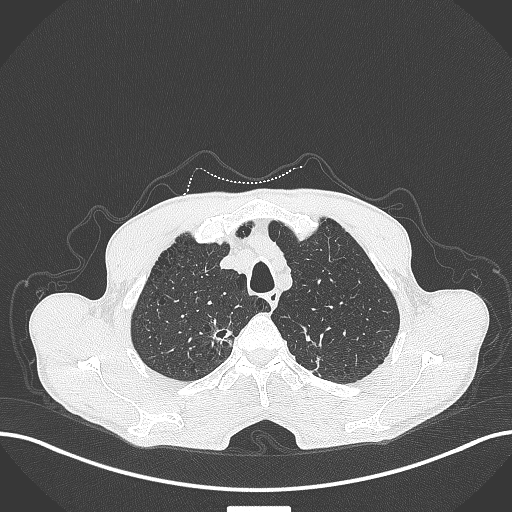
Chest CT, one axial slice. Slice 360 of 445 in the series (ordered by position). Reconstruction kernel B70f. 120 kVp. Lung window (W 1500 / L -600 HU). 512 × 512 image matrix, field of view 400 × 400 mm. Patient: male, 70 years. Case-level facts recorded for this patient, not image findings: clinical TNM (as recorded): T1a N0 M0.
Outlined on this slice (rectangle marked by the reading radiologist):
- lung tumour (recorded histology: adenocarcinoma): box from (x=205, y=322) to (x=234, y=347) px